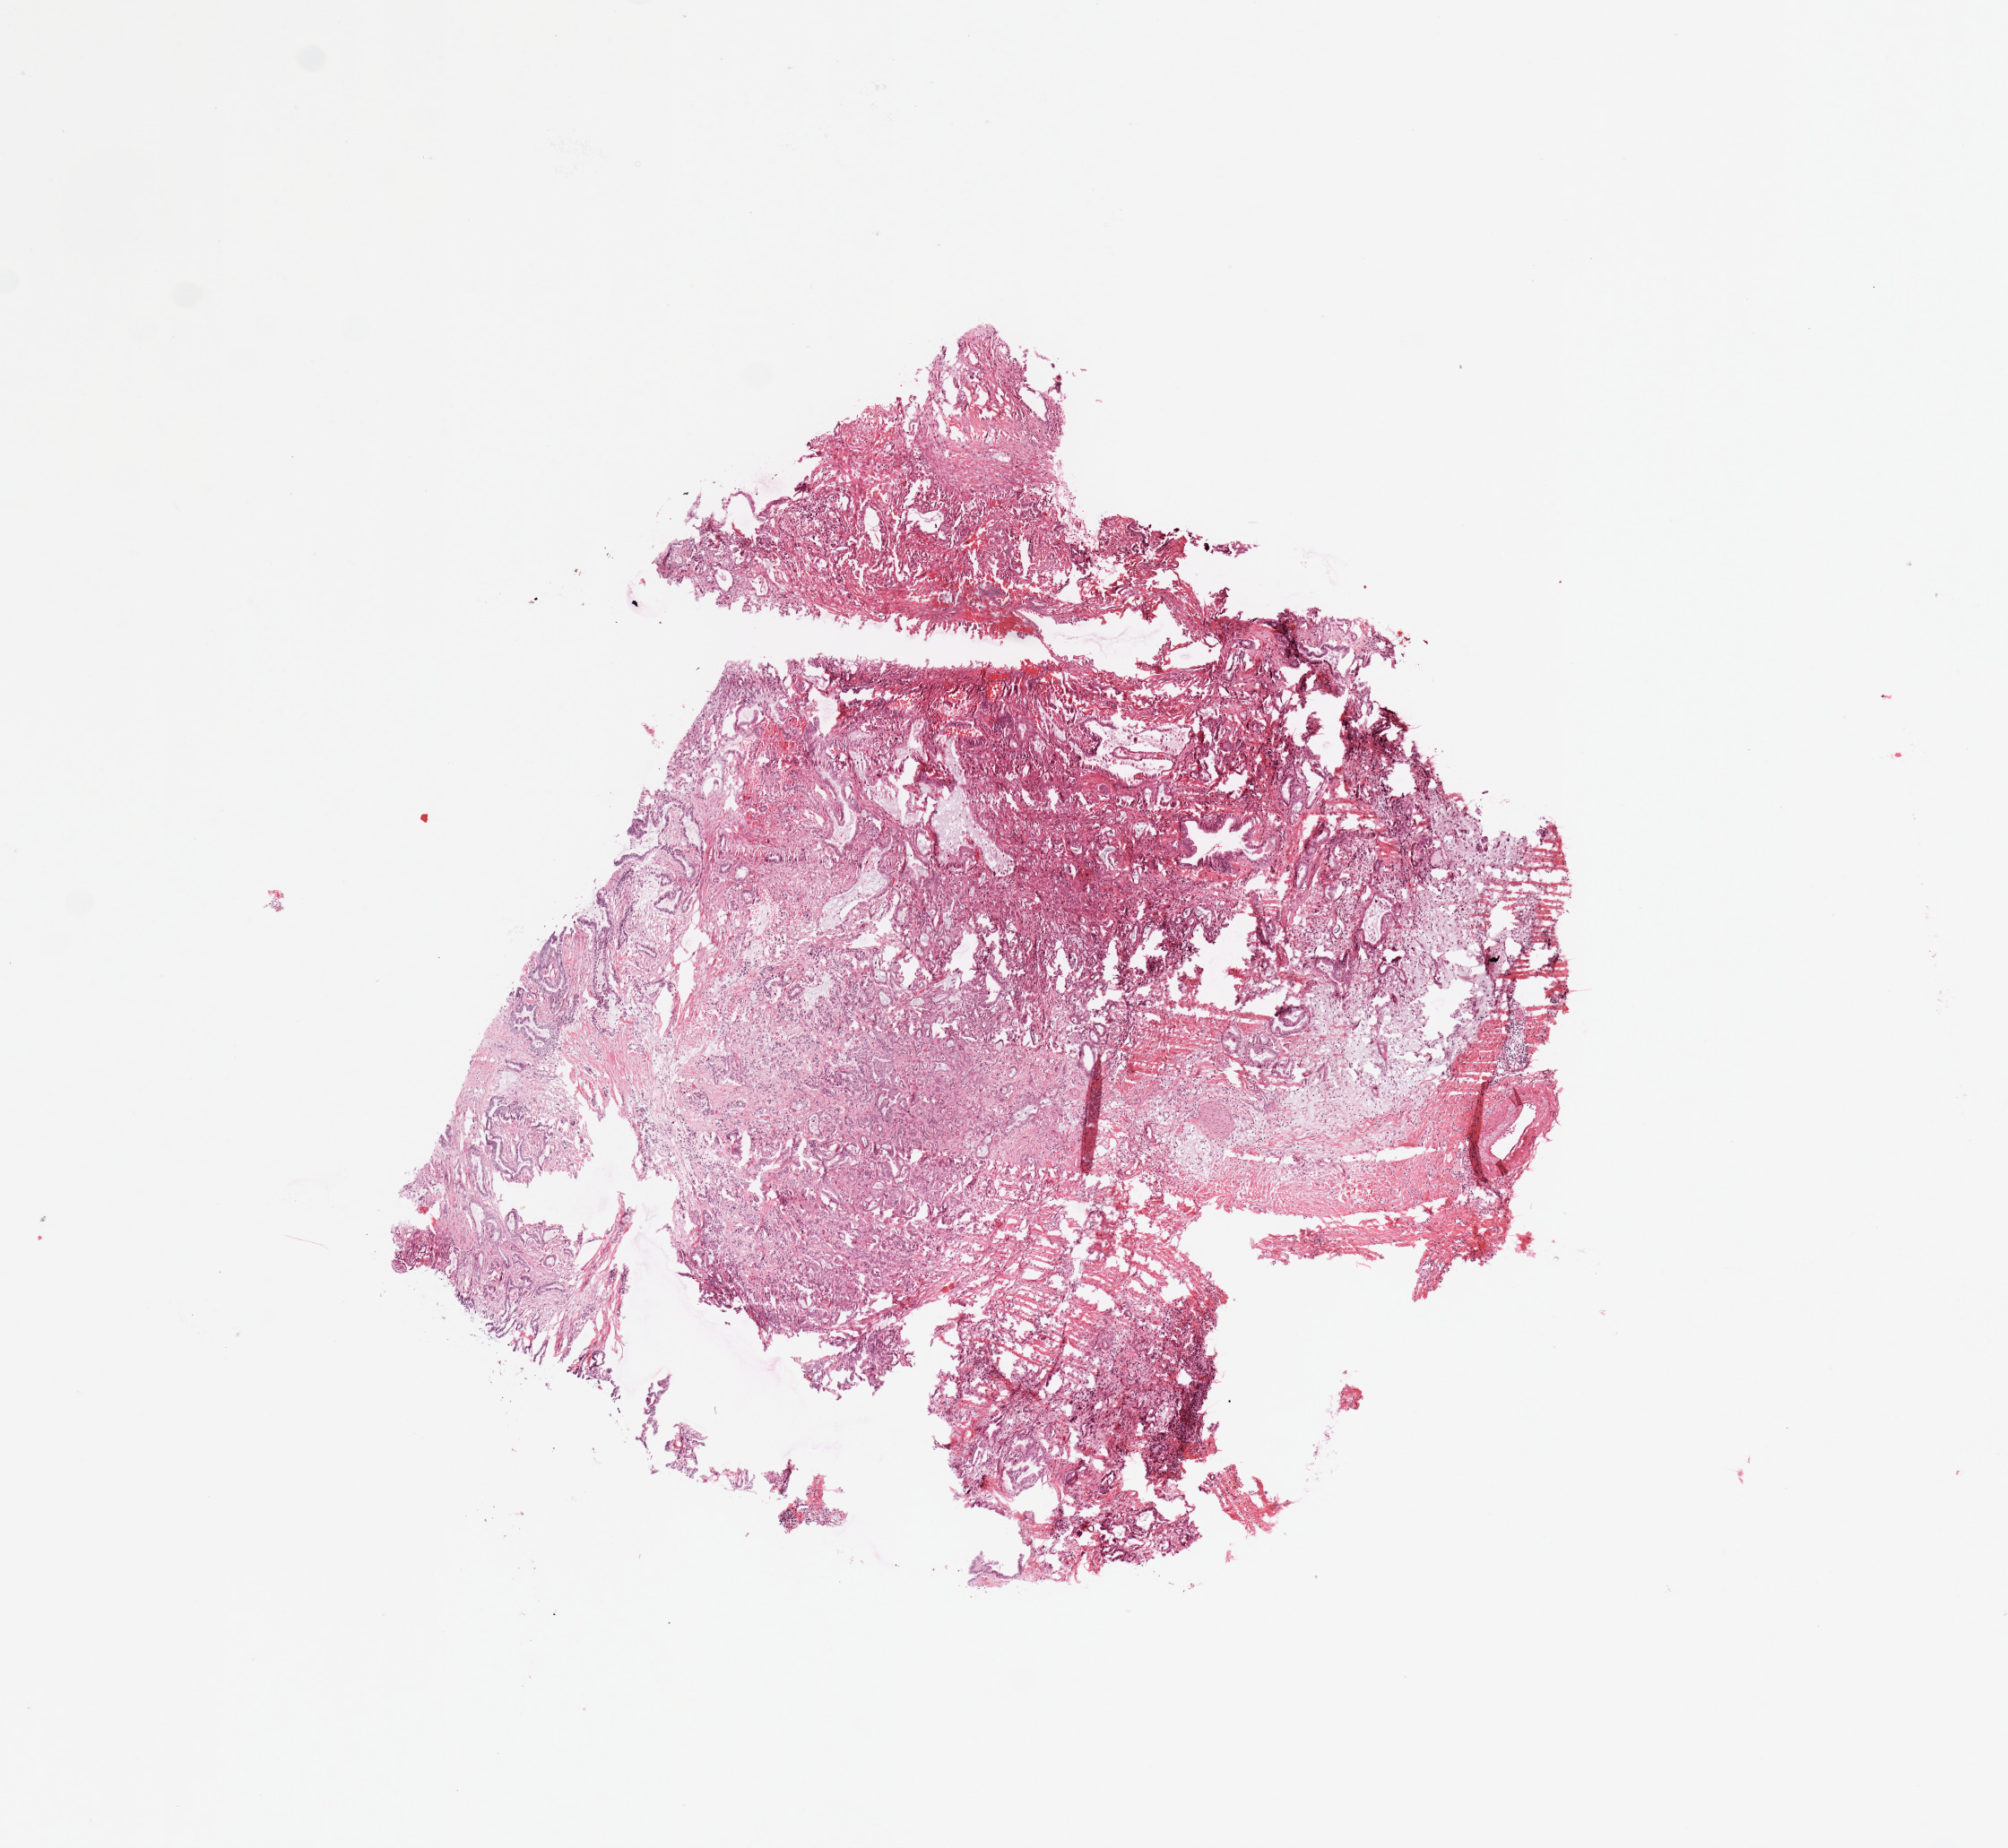
Whole-slide histology image, H&E-stained, shown as a low-resolution overview of the whole scanned area (about 8.9 x 8.2 mm, from a 20x scan); tumour tissue sample, sampled site: pancreas. Male, 42 y/o. Histologic grade: G3 (poorly differentiated). Composition of this section per pathologist review: tumour nuclei 75%, necrosis 5%.
Primary tumour site (as recorded): head. AJCC pathologic stage: III. Histologic diagnosis: Infiltrating duct carcinoma, NOS.